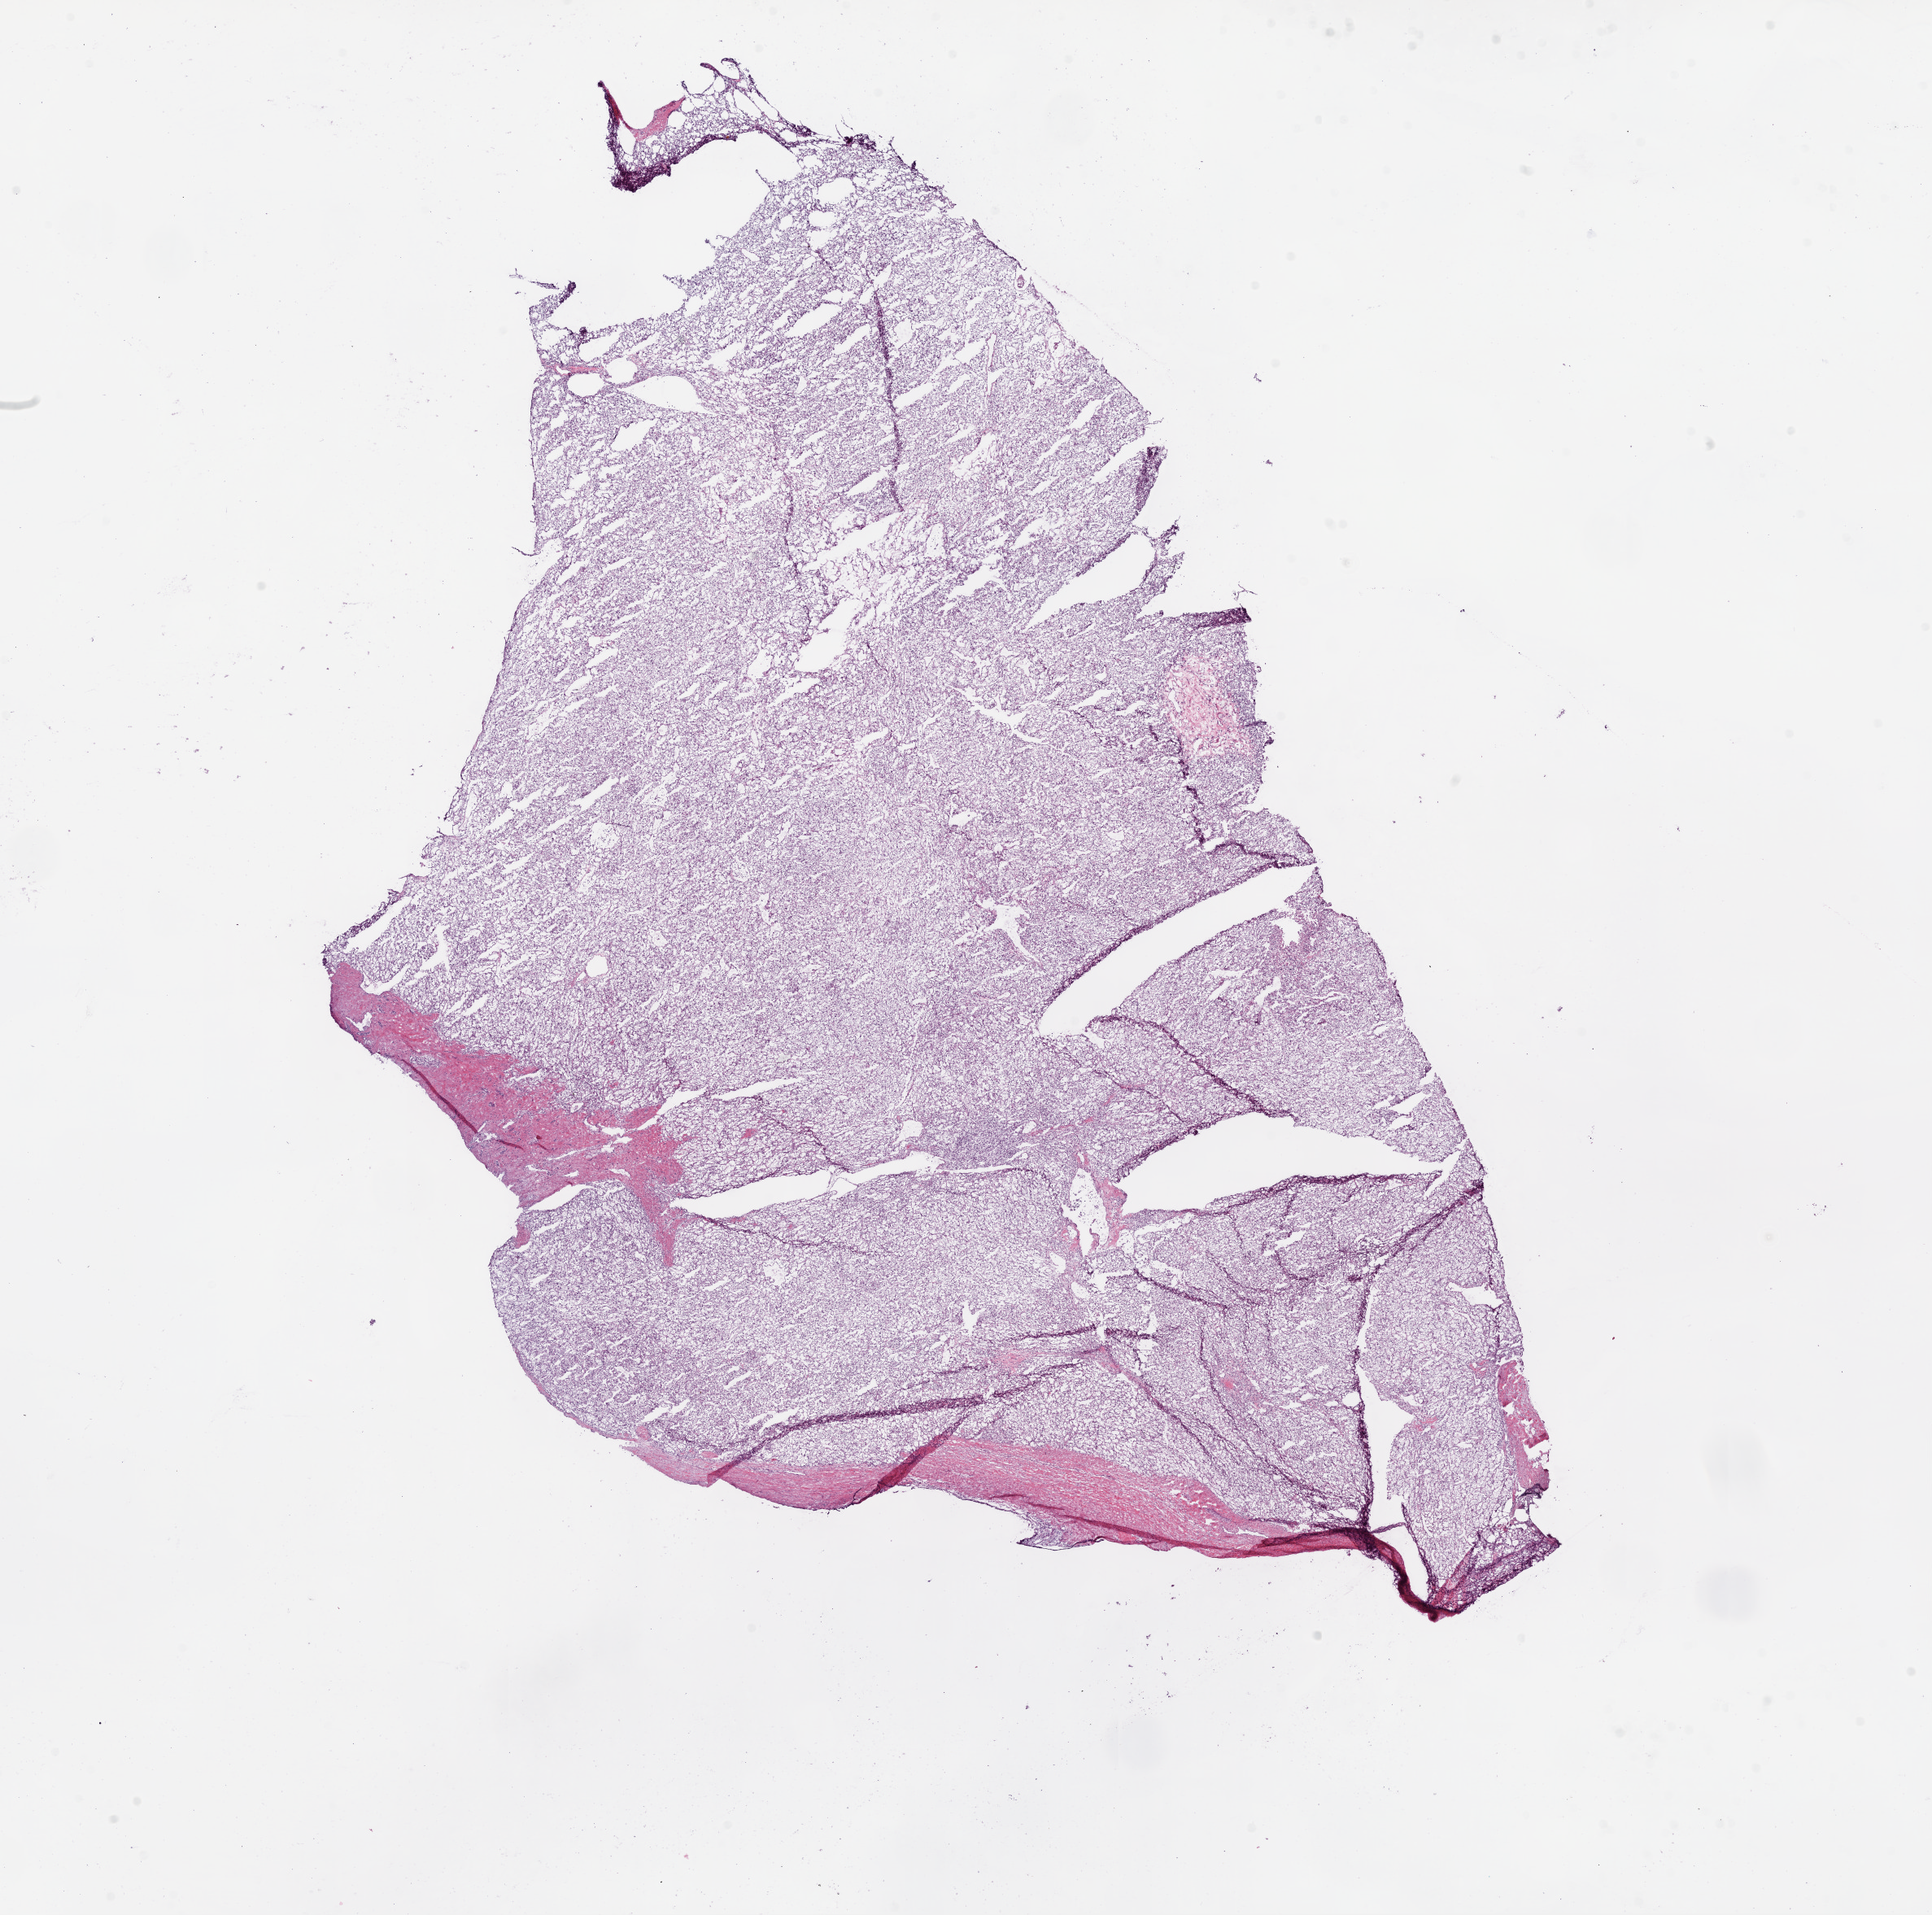
Hematoxylin and eosin (H&E) stained whole-slide image, shown as a low-resolution overview of the whole scanned area (about 19.1 x 18.9 mm); frozen section; sample: primary tumour, kidney. Male, age 75 years at initial diagnosis. Histologic grade: G2 (moderately differentiated). Slide review estimates, as recorded: tumour cells 90%, tumour nuclei 90%, normal cells 0%, stromal cells 10%, necrosis 0%.
* histologic diagnosis: Clear cell adenocarcinoma, NOS
* laterality: right
* AJCC pathologic stage: III